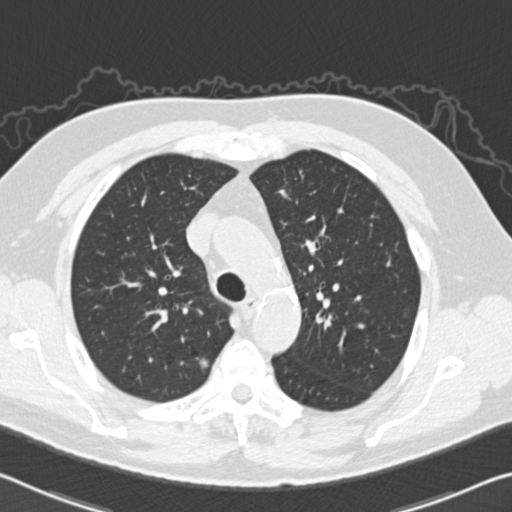
Low-dose screening chest CT, one axial slice; position 112 of 151 along the scan axis; reconstruction kernel B30f; lung window (W 1500 / L -600 HU); 512 × 512 image matrix, field of view 340 × 340 mm.
Structures marked on this image (expert manual segmentation):
- lesion 1 (tumor, upper lobe of right lung): bounding box [x1, y1, x2, y2] px = [200, 359, 208, 368]